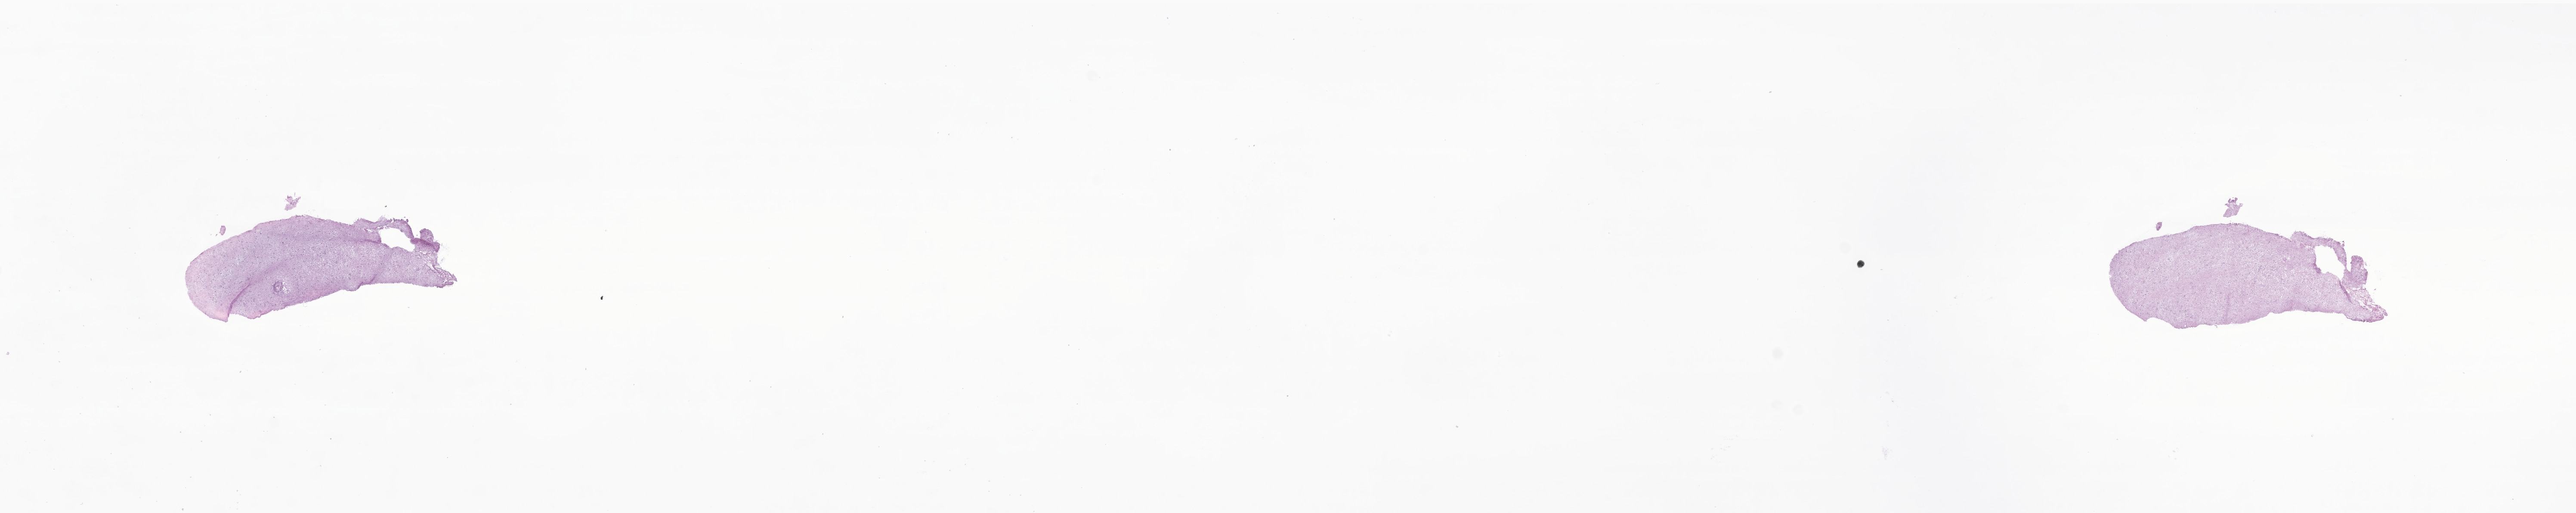
Hematoxylin and eosin (H&E) whole-slide image of tumor tissue from the brain — whole scanned area (about 25.2 x 5.0 mm) shown as a low-resolution overview; cryosection (OCT / tissue freezing medium). Patient: female, age 283 months (23 years 7 months).
- diagnosis: Glioma, malignant